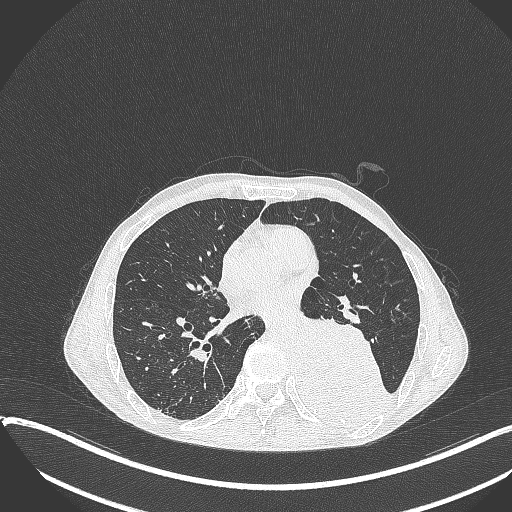
Chest CT, one axial slice. Slice 169 of 401 in the series (ordered by position). Reconstruction kernel B70f. 120 kVp. Lung window (W 1500 / L -600 HU). 1 mm slice thickness. 512 × 512 image matrix, field of view 400 × 400 mm. Patient: male, 57 years. Case-level facts recorded for this patient, not image findings: clinical TNM (as recorded): T4 N0 M0.
Structures marked on this image (bounding box drawn by a radiologist):
- lung tumour (recorded histology: squamous cell carcinoma): bounding box <287,308,393,428> (left, top, right, bottom; pixels)